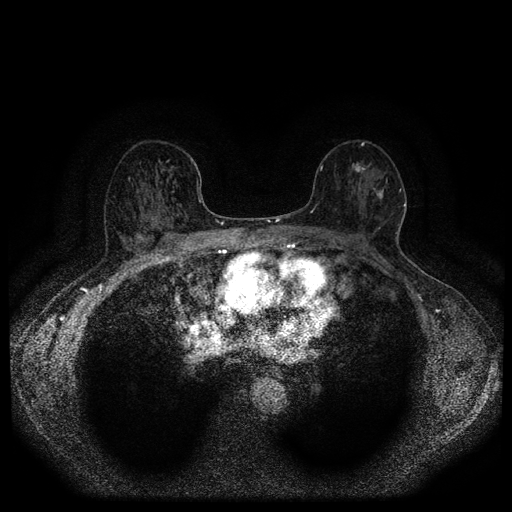
Breast MRI (dynamic contrast-enhanced, multi-phase), one axial slice. Position 61 of 116 along the scan axis. Dynamic contrast-enhanced series, time point 2 of 5 at this slice position (early post-contrast). 1.5 T. TE 2.7 ms, TR 5.4 ms. 2 mm slice thickness. 512 × 512 image matrix, field of view 330 × 330 mm. Female patient, age 56 years.
Annotated regions visible in this slice (semi-automatic segmentation, software-assisted and operator-edited):
- breast lesion (labelled 'tumour' in the annotation; benign lesions carry a separate 'benign' label): bounding box (x1, y1, x2, y2) in pixels: (371, 177, 390, 205)